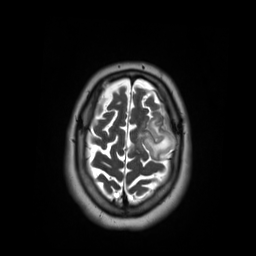
Brain MRI from a brain-tumour surgery series, one axial slice. 3.03 mm slice thickness. 256 × 256 image matrix, field of view 250 × 250 mm. From the clinical record (not read from this slice): histopathology: Oligodendroglioma; WHO grade: 2; IDH mutation: yes.
Annotated regions visible in this slice (manually delineated by an expert):
- tumour: bounding box (x1, y1, x2, y2) in pixels: (139, 118, 180, 160)